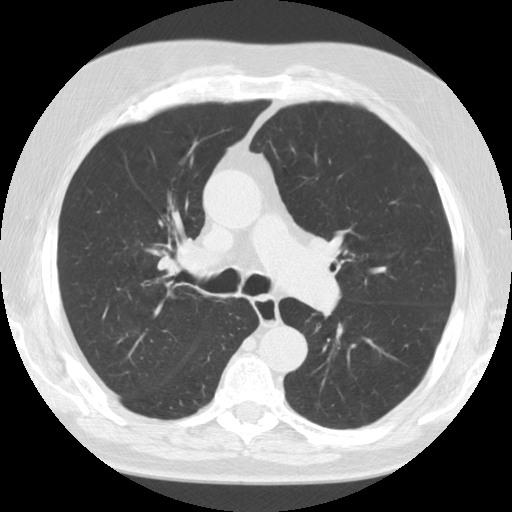
Low-dose screening chest CT, axial slice, baseline screening round, lung window (W 1500 / L -600 HU), 2.5 mm slice thickness, standard (soft-tissue) reconstruction kernel (STANDARD), slice 47 of 125 in the series, 512 × 512 image matrix. Male participant, aged 72 years at enrolment. Former smoker at enrolment.
Expert-annotated lung lesion, bounding box (x1, y1, x2, y2) in pixels: (139, 220, 218, 298). Screening reader's record for this exam: no non-calcified nodule ≥4 mm recorded. Official screen result: negative screen, minor abnormalities not suspicious for lung cancer. Later outcome: lung cancer diagnosed 779 days after this screen (after the third annual screen) — small cell carcinoma, NOS, right upper lobe, stage IV (AJCC 6th edition), 7 mm at pathology.